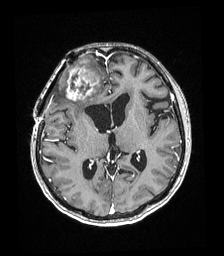
Brain MRI from a brain-tumour surgery series, one axial slice; position 96 of 192 along the scan axis; T1-weighted post-contrast; 1 mm slice thickness; 224 × 256 image matrix, field of view 219 × 250 mm. From the clinical record (not read from this slice): histopathology: Astrocytoma; WHO grade: 4; IDH mutation: yes; tumour location: Right superficial frontal.
Structures marked on this image (manually delineated by an expert):
- tumour: bounding box <66,59,100,102> (left, top, right, bottom; pixels)